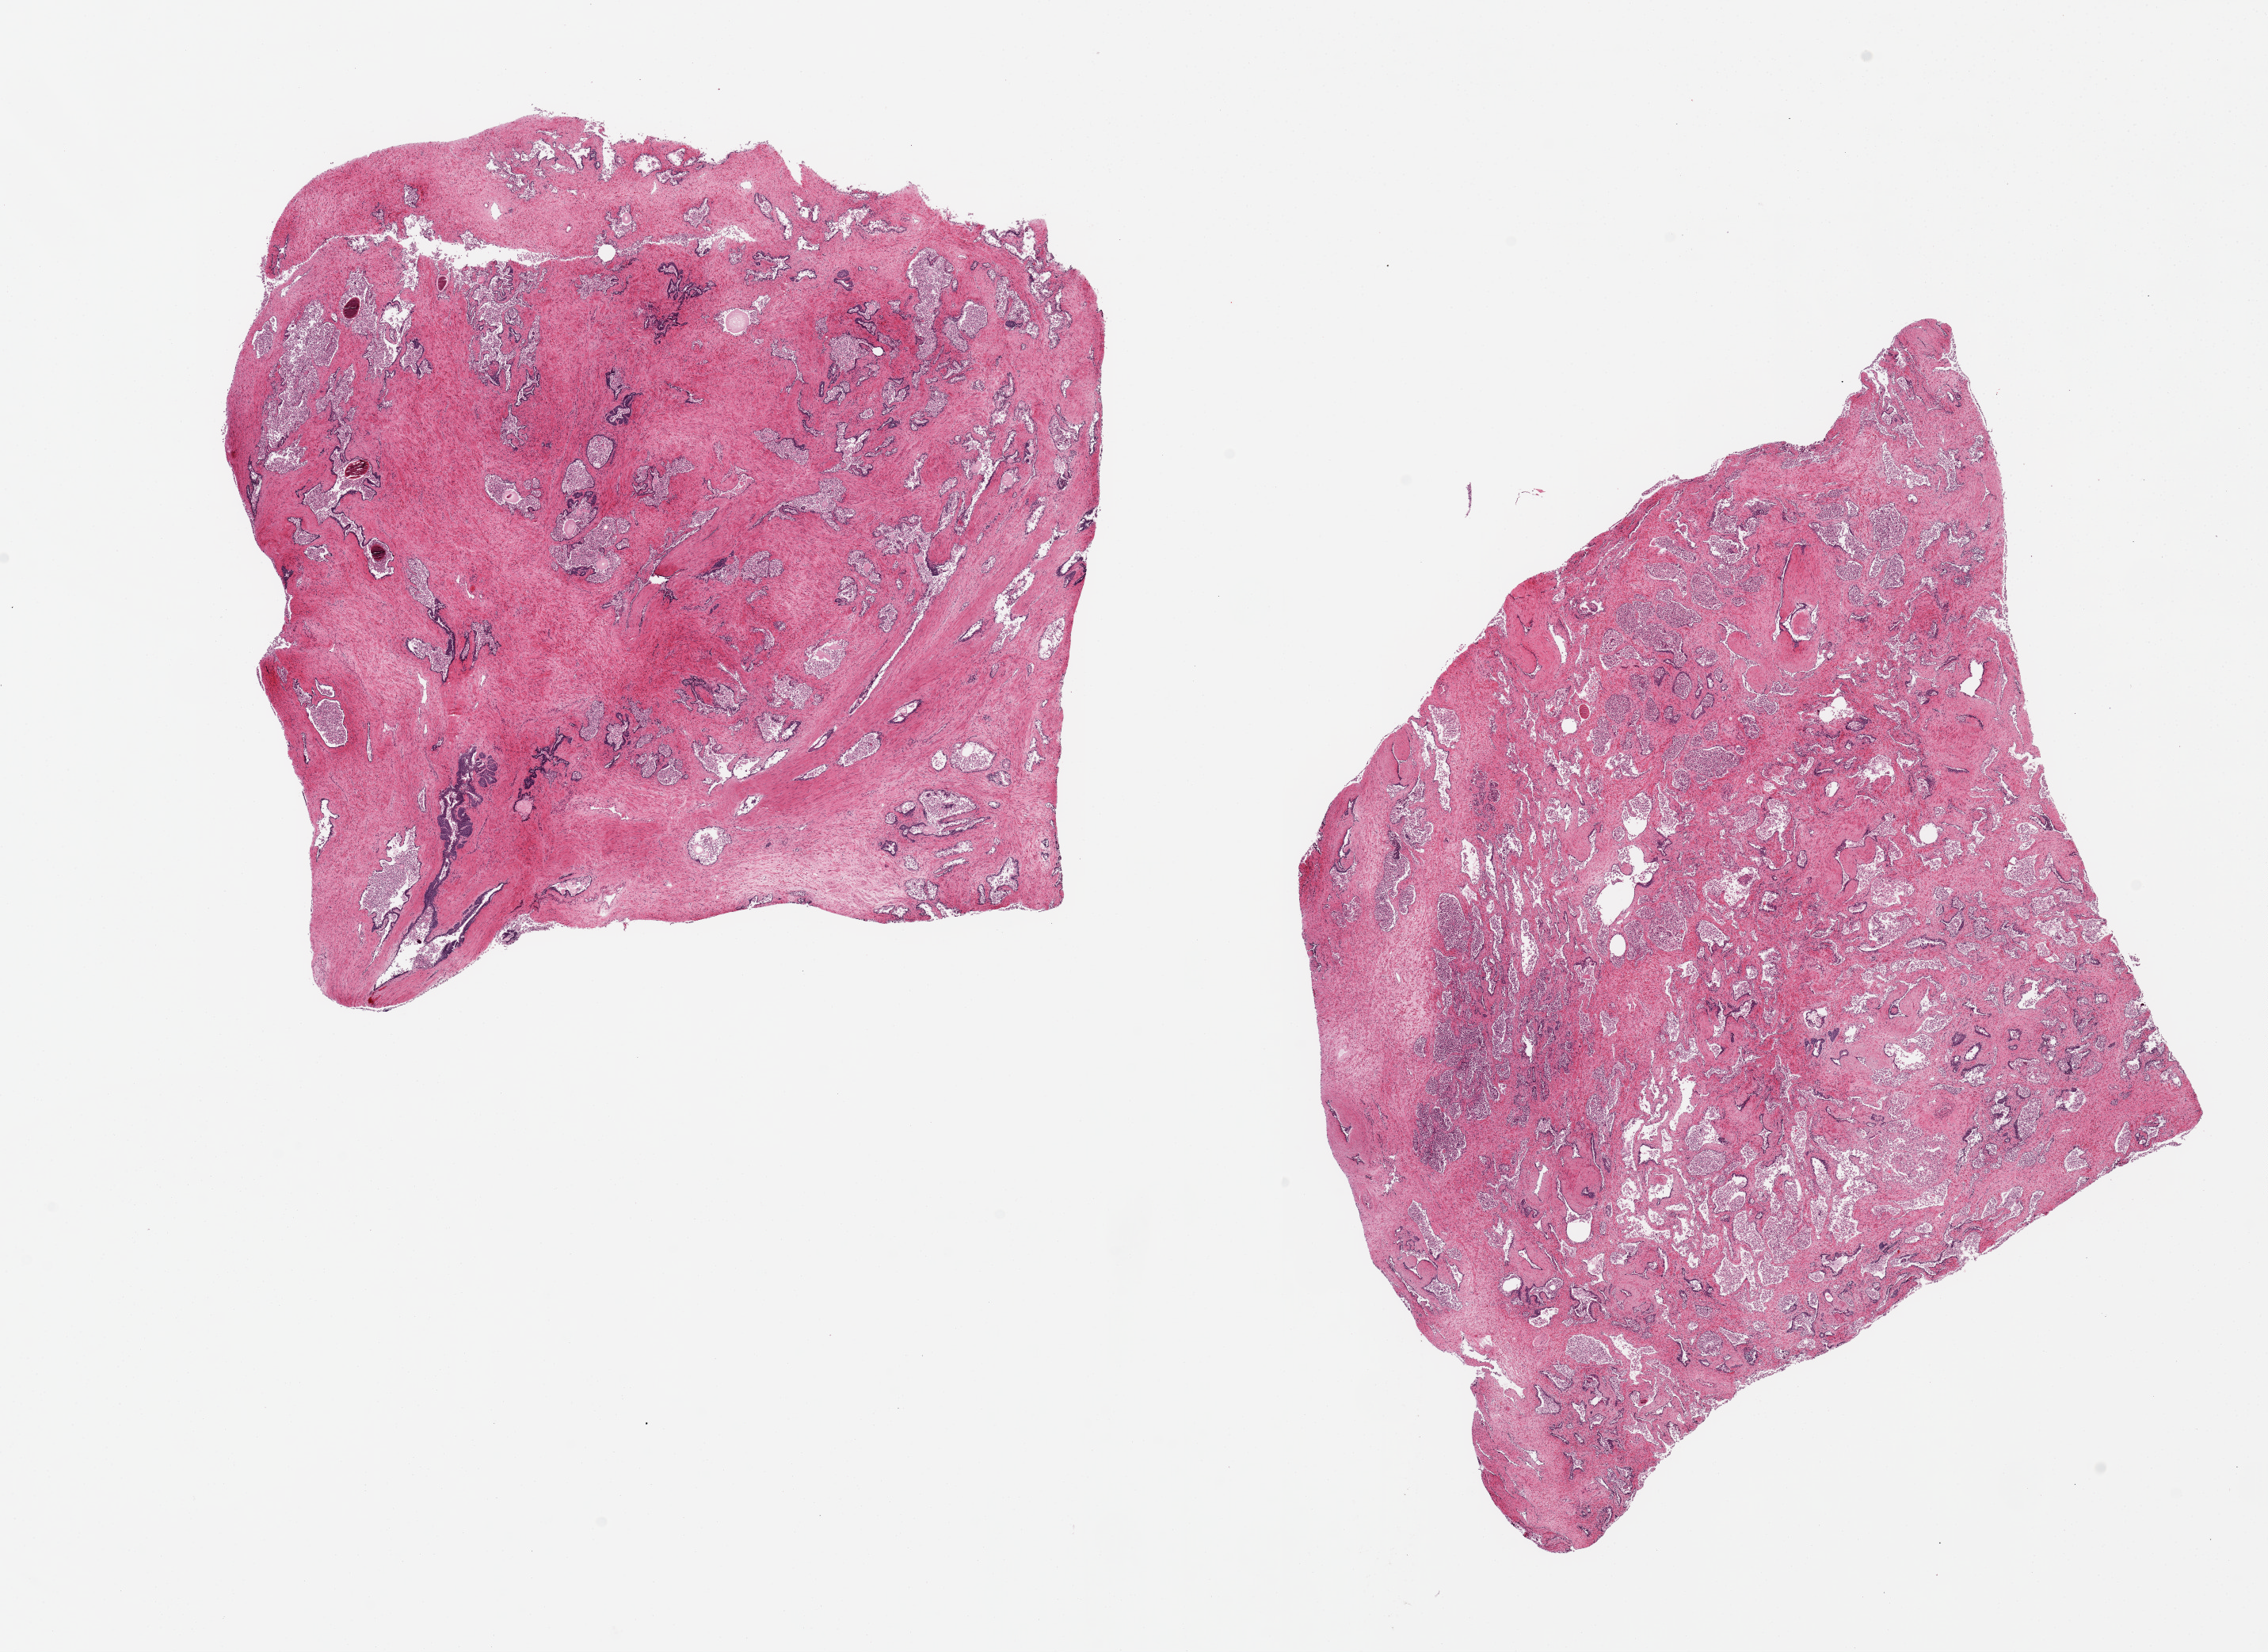
Digitized hematoxylin and eosin (H&E)-stained section — a low-resolution overview of the entire scanned area, about 22.6 x 16.5 mm. PAXgene-fixed, paraffin-embedded tissue. Sampled site (target tissue): prostate. Tissue donor sample. Male donor.
* pathologist's review note for this sample: 2 pieces 9x9 & 9x8mm; glands badly autolyzed